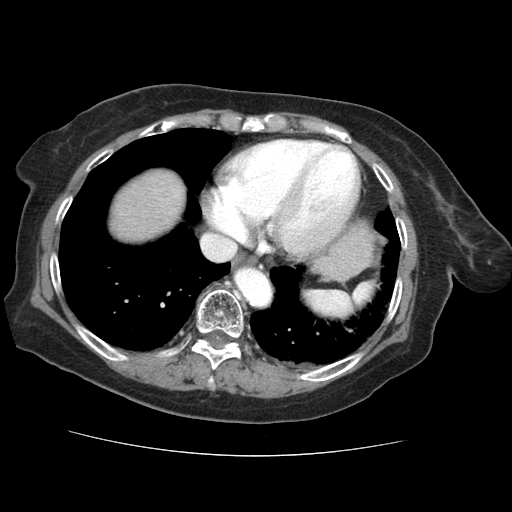
Contrast-enhanced abdominal CT (liver protocol), one axial slice; slice 61 of 73 in the series (ordered by position); soft-tissue window (W 400 / L 40 HU); 512 × 512 image matrix, field of view 360 × 360 mm. Case-level facts recorded for this patient, not image findings: diagnosis: hepatocellular carcinoma (patient treated with transarterial chemoembolisation; whether this scan precedes or follows treatment is not stated here); TNM stage (as recorded): Stage-IVB; Child-Pugh class: A; tumour nodularity: uninodular.
Outlined on this slice (semi-automatic segmentation, software-assisted and operator-edited):
- liver parenchyma outside the tumour (the mass and vessels are separate outlines, so this box may not span the whole liver): bounding box (x1, y1, x2, y2) in pixels: (112, 170, 184, 240)